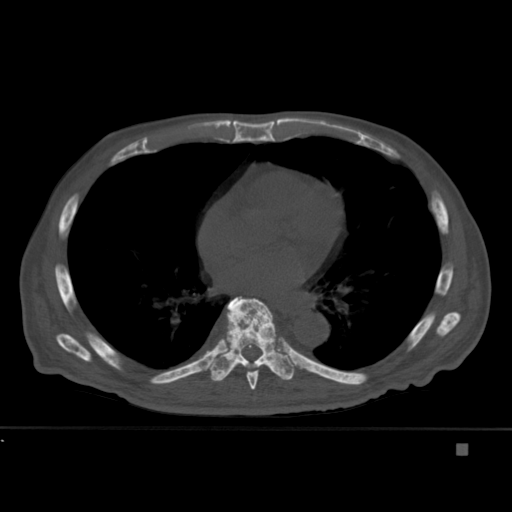
CT including the spine, one axial slice. Position 269 of 451 along the scan axis. Bone window (W 1800 / L 400 HU). 1.5 mm slice thickness. 512 × 512 image matrix, field of view 378 × 378 mm. Male patient, age 75 years. From the clinical record (not read from this slice): primary cancer: prostate.
Structures marked on this image (semi-automatically segmented with operator editing):
- T7 vertebra: bounding box (x1, y1, x2, y2) in pixels: (246, 299, 276, 390)
- T8 vertebra: (208, 296, 295, 382)